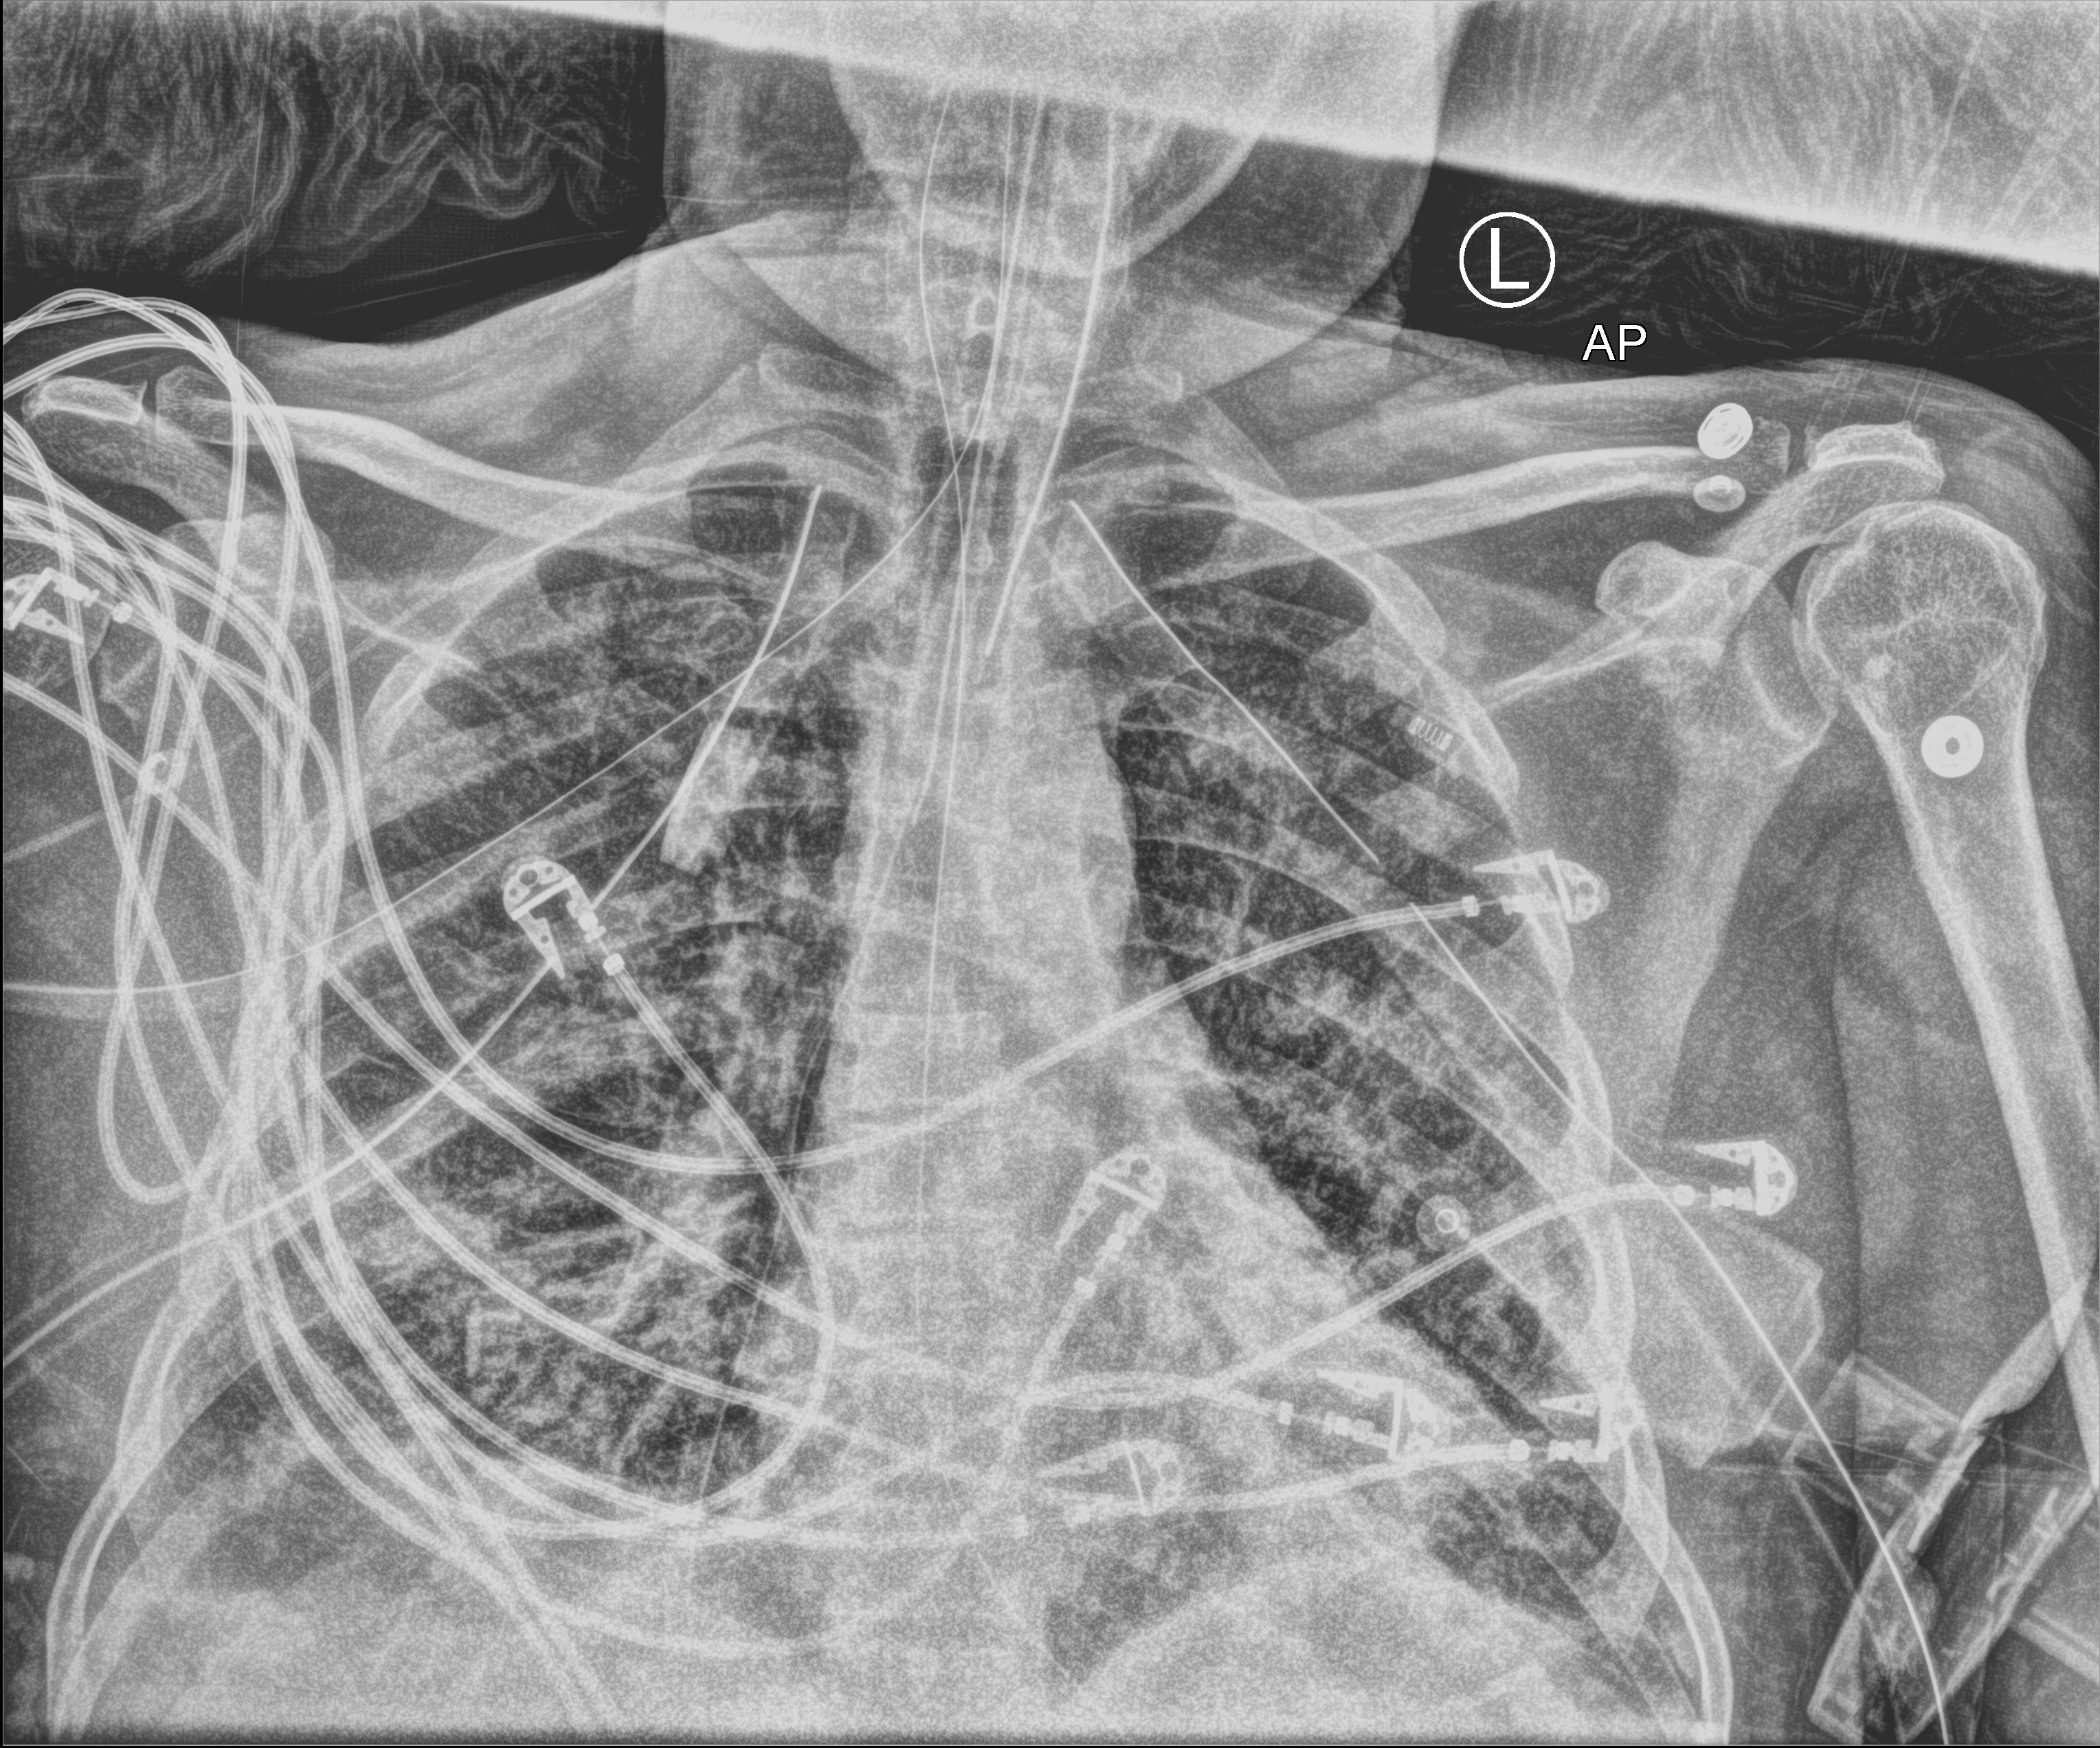
Chest X-ray (portable); anteroposterior (AP) projection. Male patient hospitalised with COVID-19, age 18–59 years.
Hospital-stay facts (about this admission, not read from this image; timing relative to this image not recorded): mechanically ventilated during this hospital stay: yes; length of hospital stay: 83 days; COPD (admission record): no.